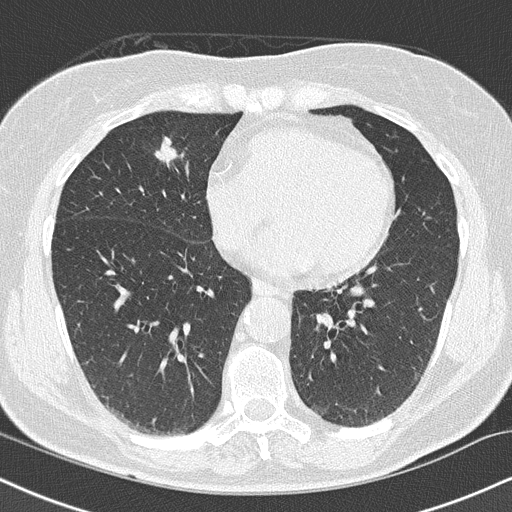
Chest CT (low-dose screening protocol), one axial image, baseline annual screen, lung window (W 1500 / L -600 HU), 2 mm slice thickness, 512 × 512 image matrix. Female, age 66 years at enrolment. Current smoker at enrolment.
Expert-annotated lung lesion, bounding box [x1, y1, x2, y2] px = [145, 130, 181, 165]. Screening reader's record for this exam (one nodule recorded; not confirmed to be the boxed lesion): non-calcified nodule or mass ≥4 mm, right lower lobe, 10 × 8 mm, smooth margins, soft tissue attenuation. Lung cancer was diagnosed 96 days after this screen: squamous cell carcinoma, keratinizing, NOS, right upper lobe, right middle lobe, poorly differentiated (G3), stage IA (AJCC 6th edition), 14 mm at pathology.